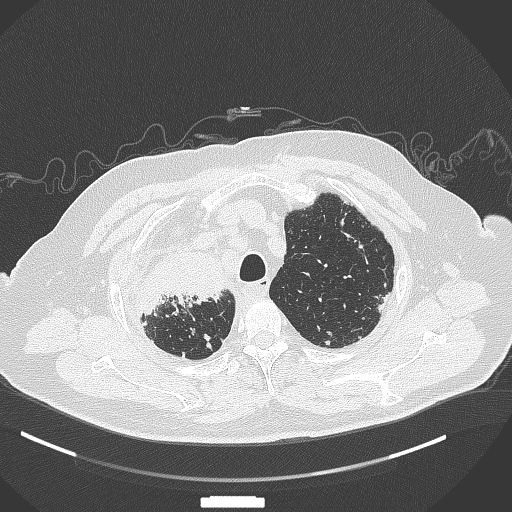
Chest CT, one axial slice; 120 kVp; lung window (W 1500 / L -600 HU); 1 mm slice thickness; 512 × 512 image matrix. Patient: male, 69 years. Case-level facts recorded for this patient, not image findings: clinical TNM (as recorded): T4 N3 M1.
Annotated regions visible in this slice (bounding box drawn by a radiologist):
- lung tumour (recorded histology: adenocarcinoma): bounding box (x1, y1, x2, y2) in pixels: (130, 243, 225, 314)